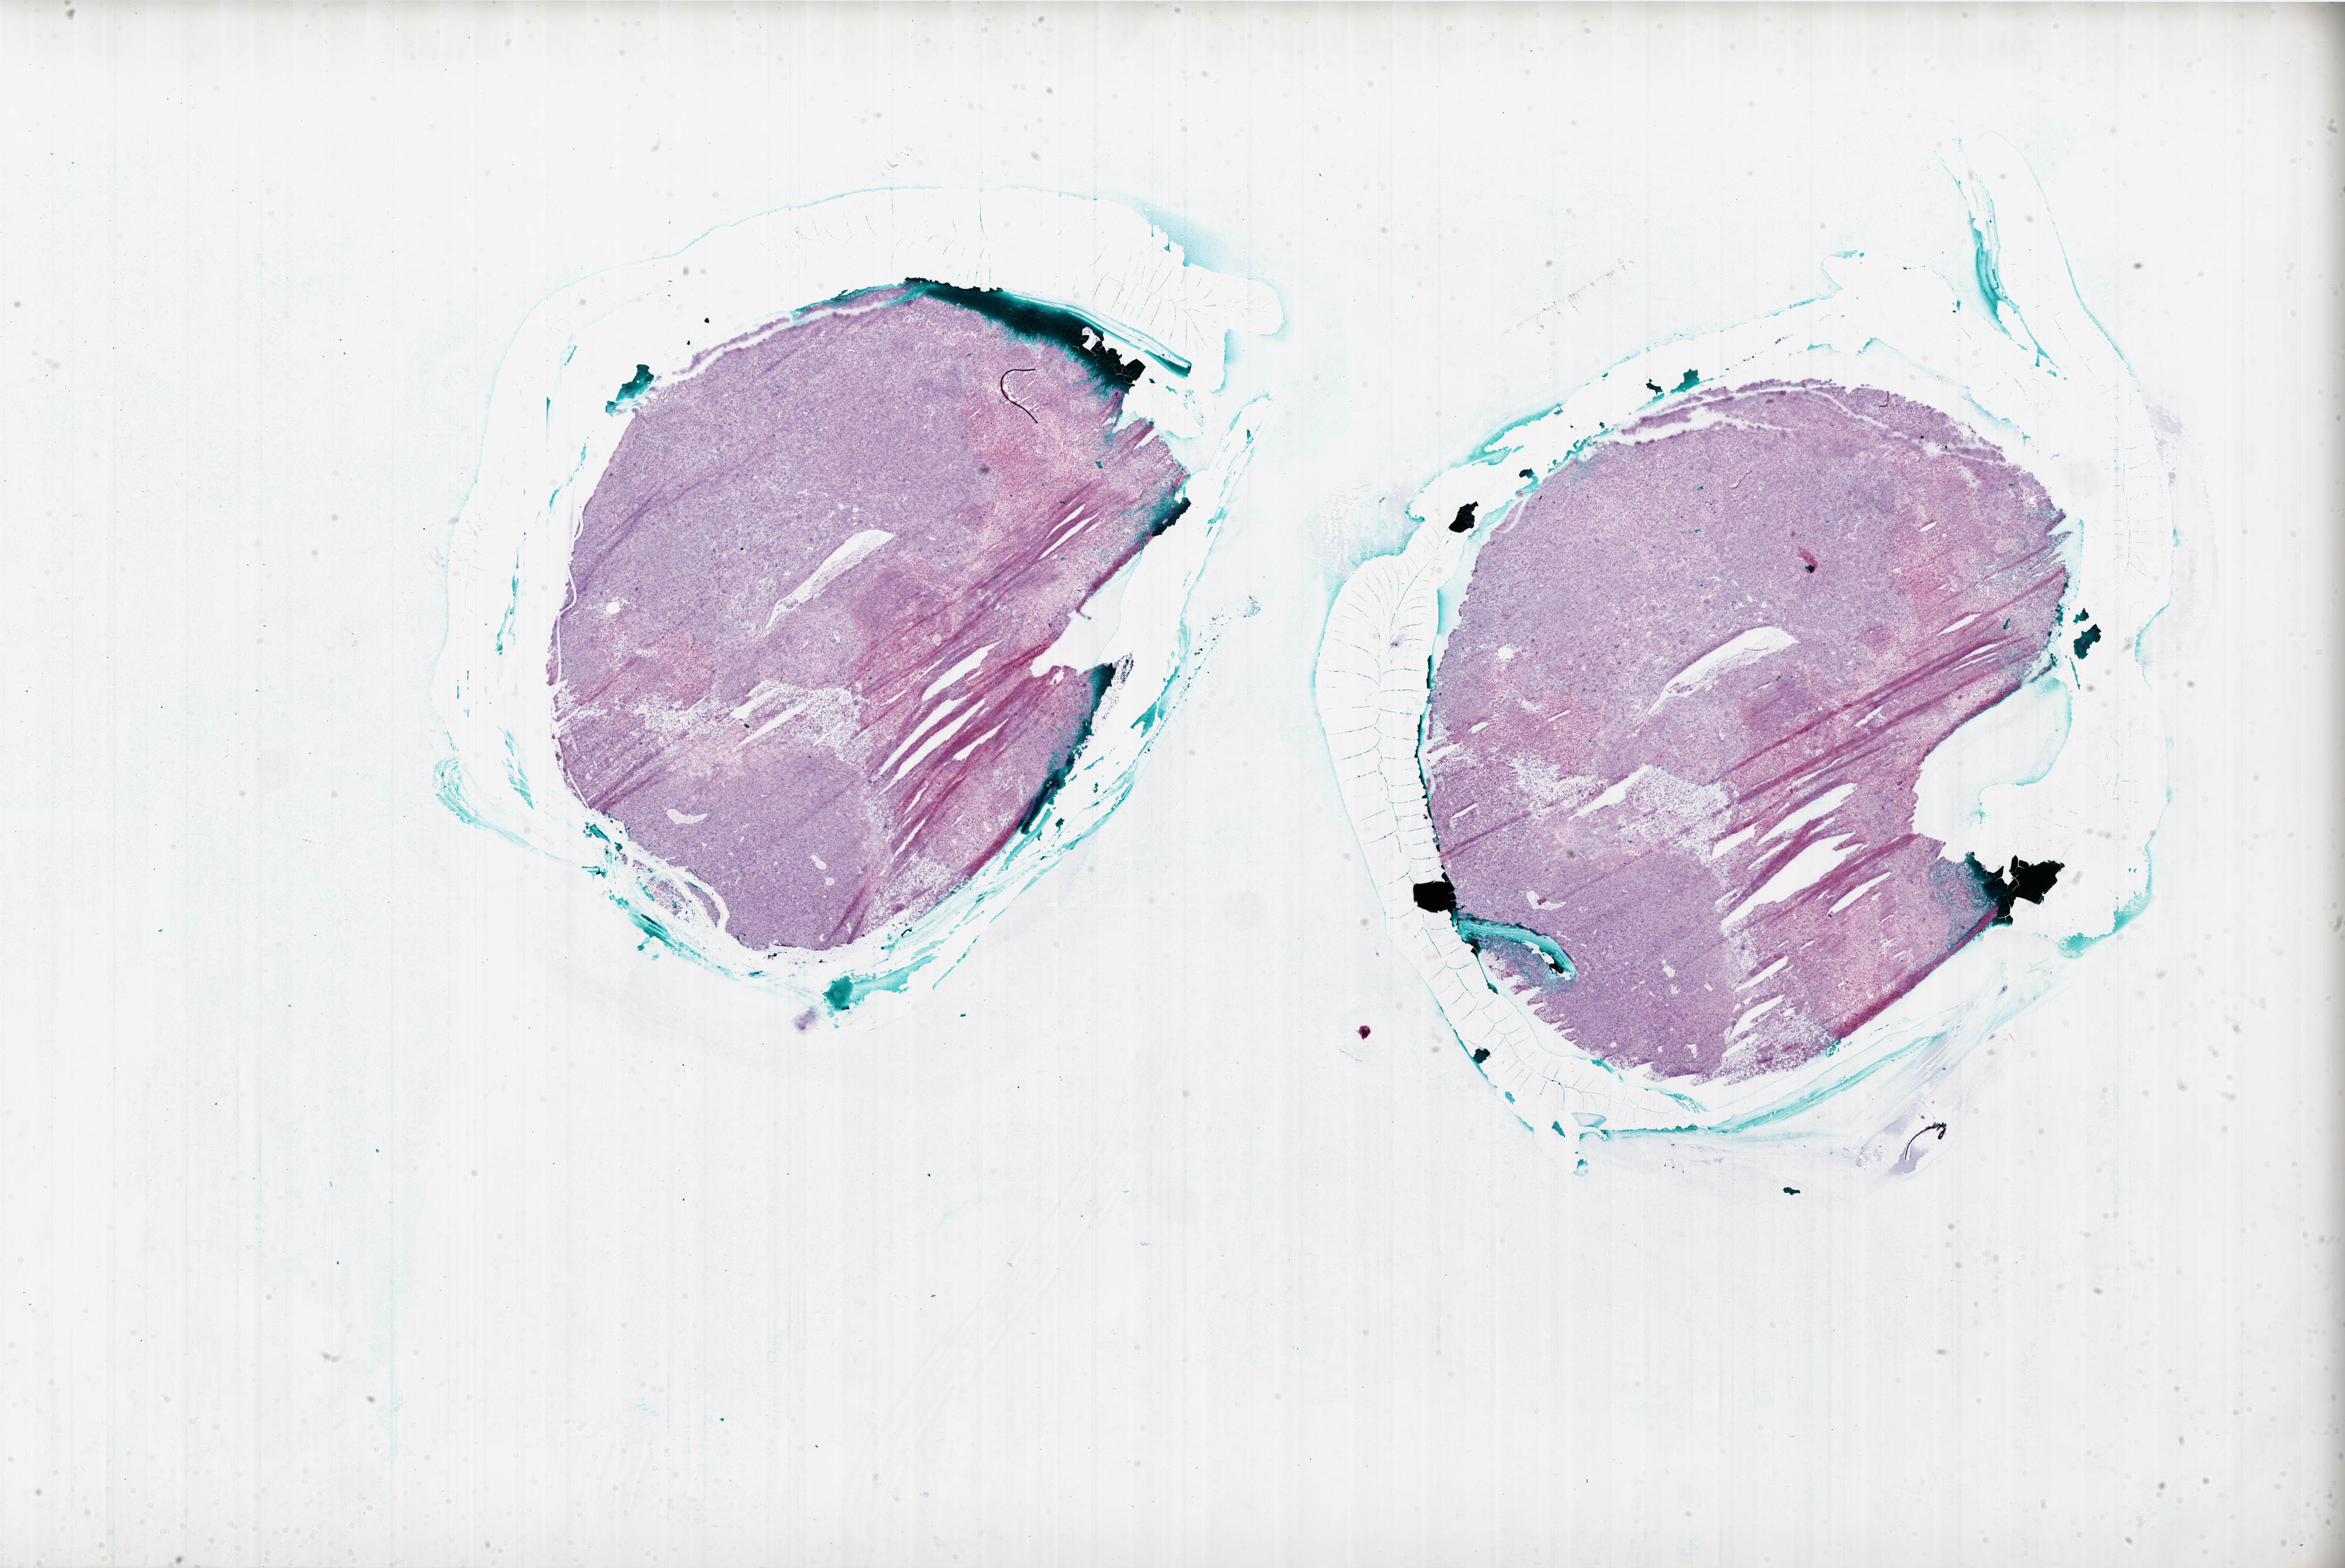
Digitized Hematoxylin and eosin (H&E) stained tissue section (whole slide), shown as a low-resolution overview of the whole scanned area (about 32.0 x 21.4 mm); frozen section; brain, primary tumour sample. Male, age 34 years at initial diagnosis. Composition of this section per pathologist review: tumour cells 55%, tumour nuclei 95%, normal cells 0%, stromal cells 5%, necrosis 40%.
Histologic diagnosis: Glioblastoma.